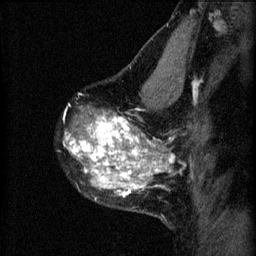
Breast MRI (dynamic contrast-enhanced), one sagittal slice. Slice 42 of 60 in the series (ordered by position). 3 images stored at this slice position (order not interpretable as contrast timing). 1.5 T. TE 4.2 ms, TR 8.2 ms. 2 mm slice thickness. 256 × 256 image matrix, field of view 180 × 180 mm. Patient: female, 40 years.
Structures marked on this image (semi-automatically segmented with operator editing):
- analysis volume of interest (the breast-tissue region the enhancement analysis was run in; not a lesion): bounding box <64,76,179,219> (left, top, right, bottom; pixels)
- tumour enhancement mask (voxels above the 70 % enhancement threshold inside the analysis volume of interest): <64,114,175,197>